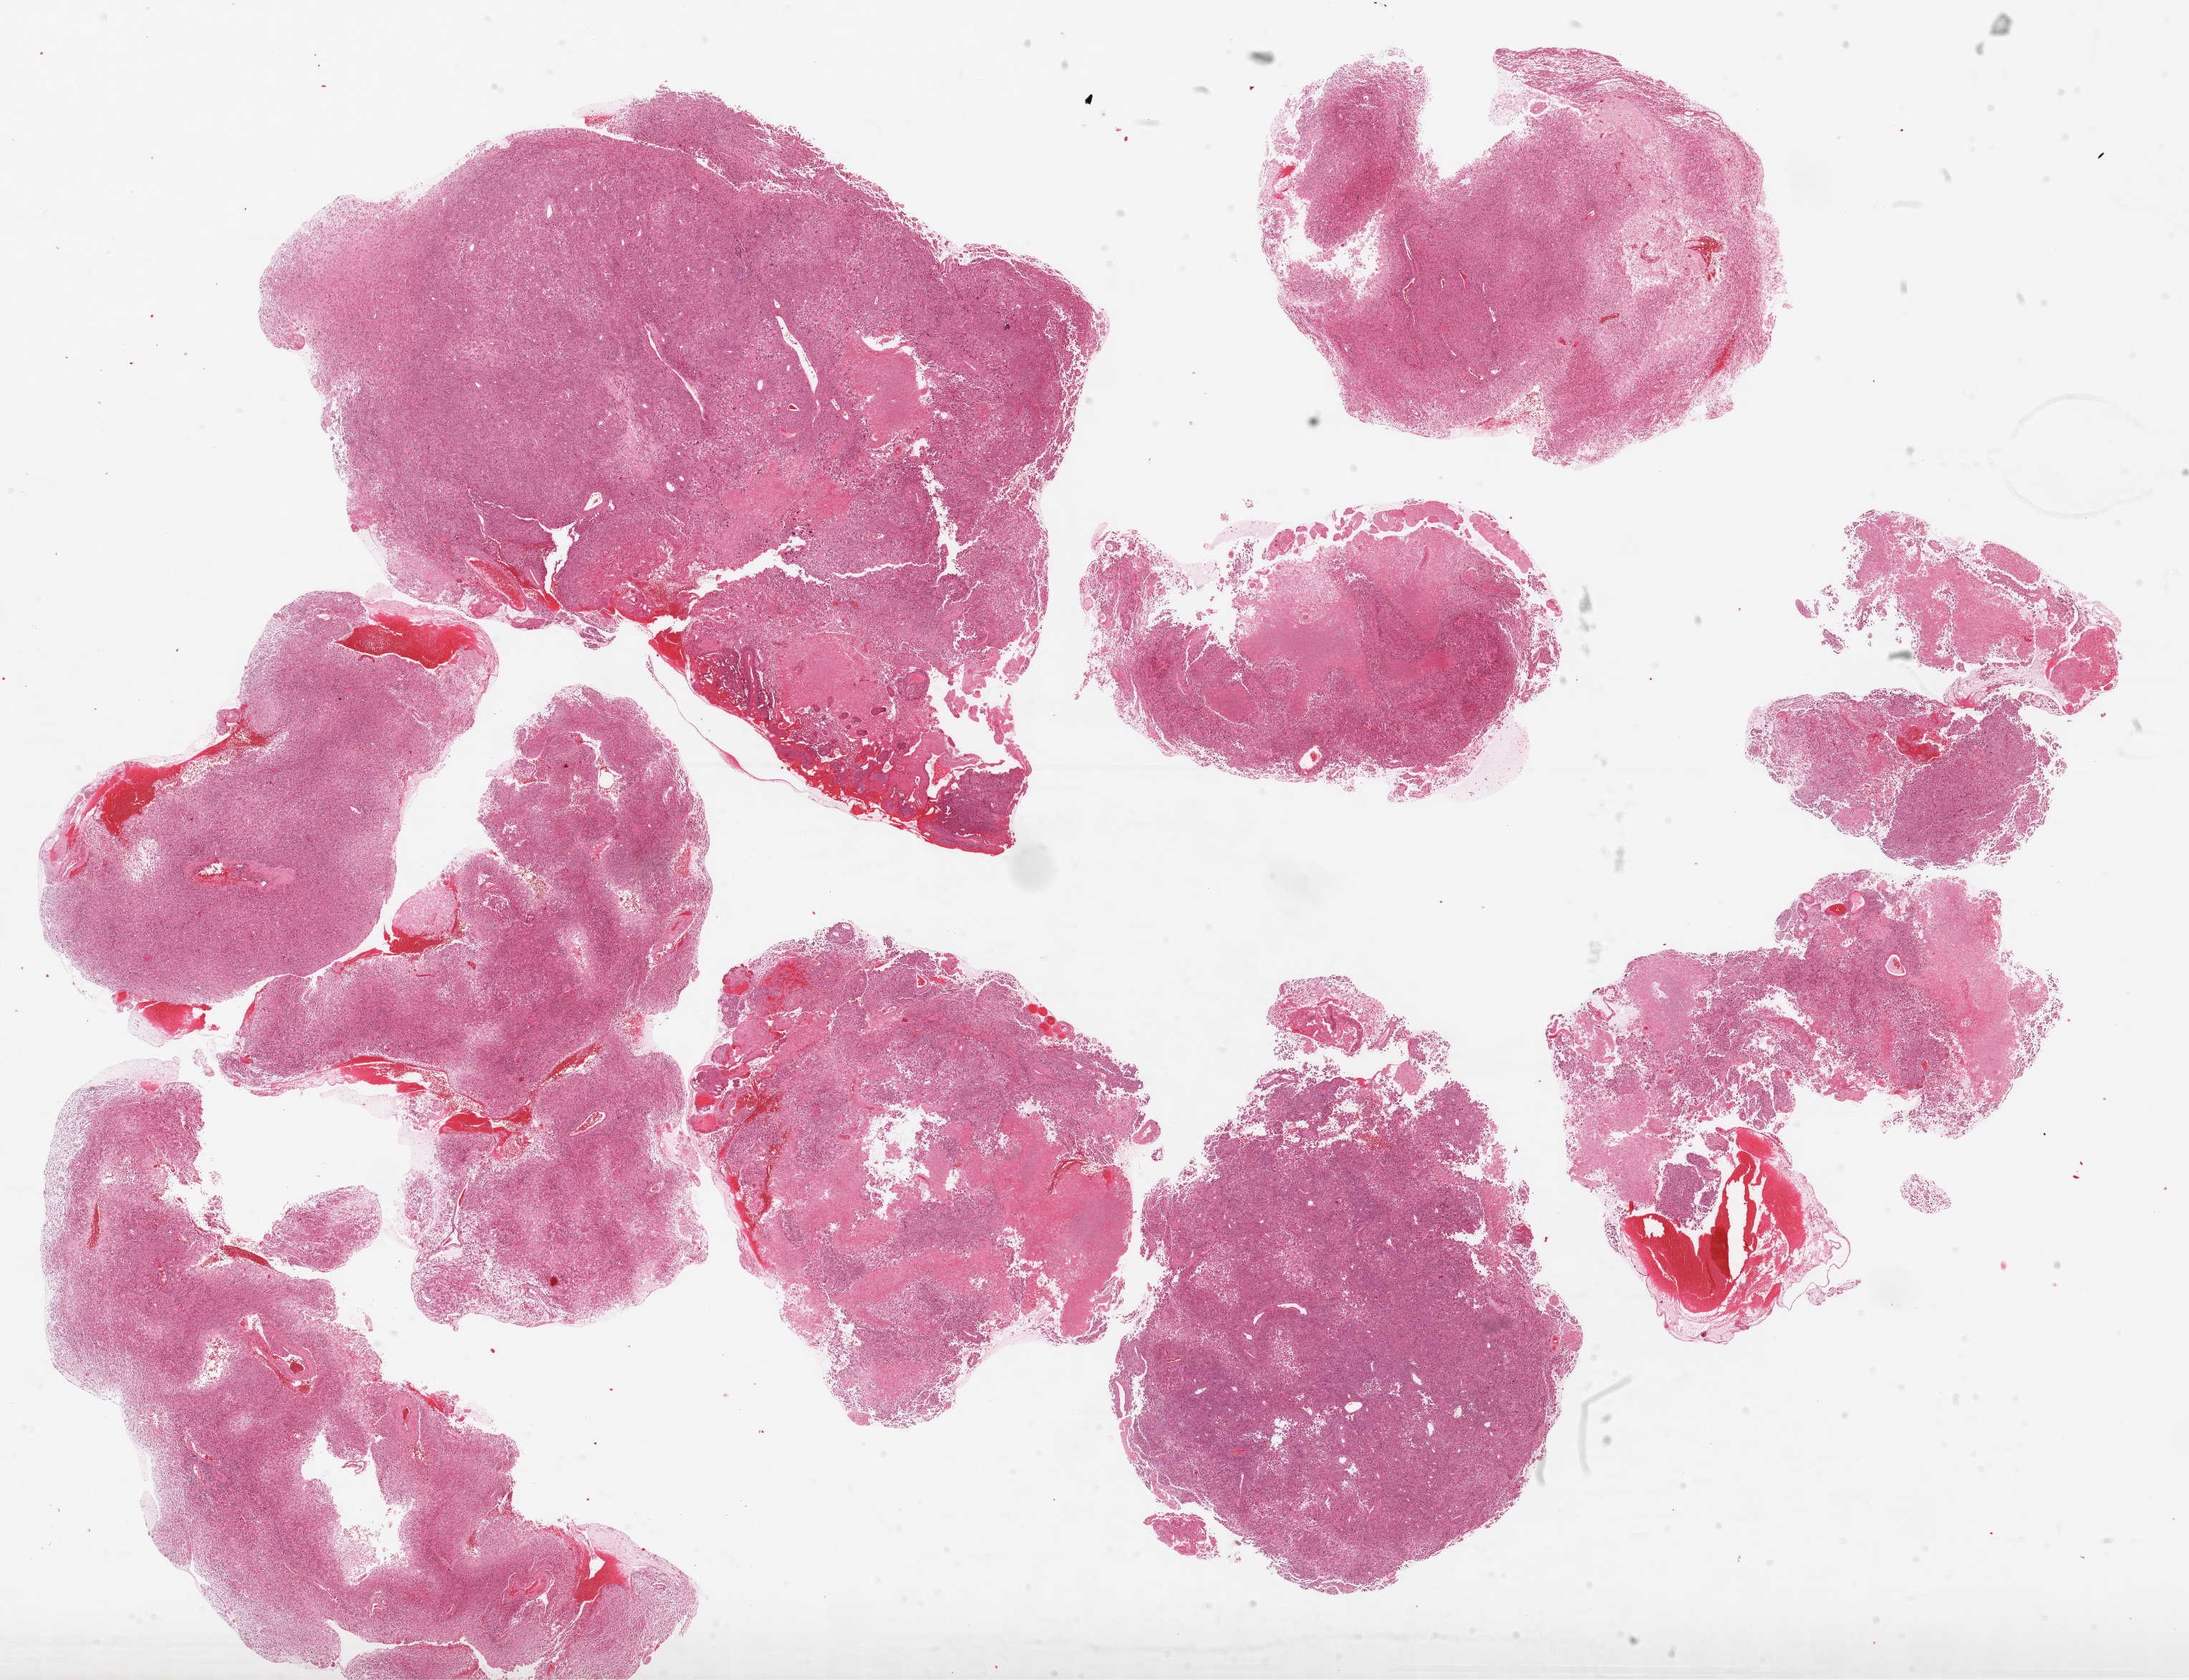
Digitized H&E tissue section (whole slide) — low-resolution overview of the scanned area, about 24.7 x 18.9 mm, formalin-fixed paraffin-embedded (FFPE) diagnostic section, primary tumour sample from the brain. Male, age 78 years at initial diagnosis.
Pathologic diagnosis: Glioblastoma.